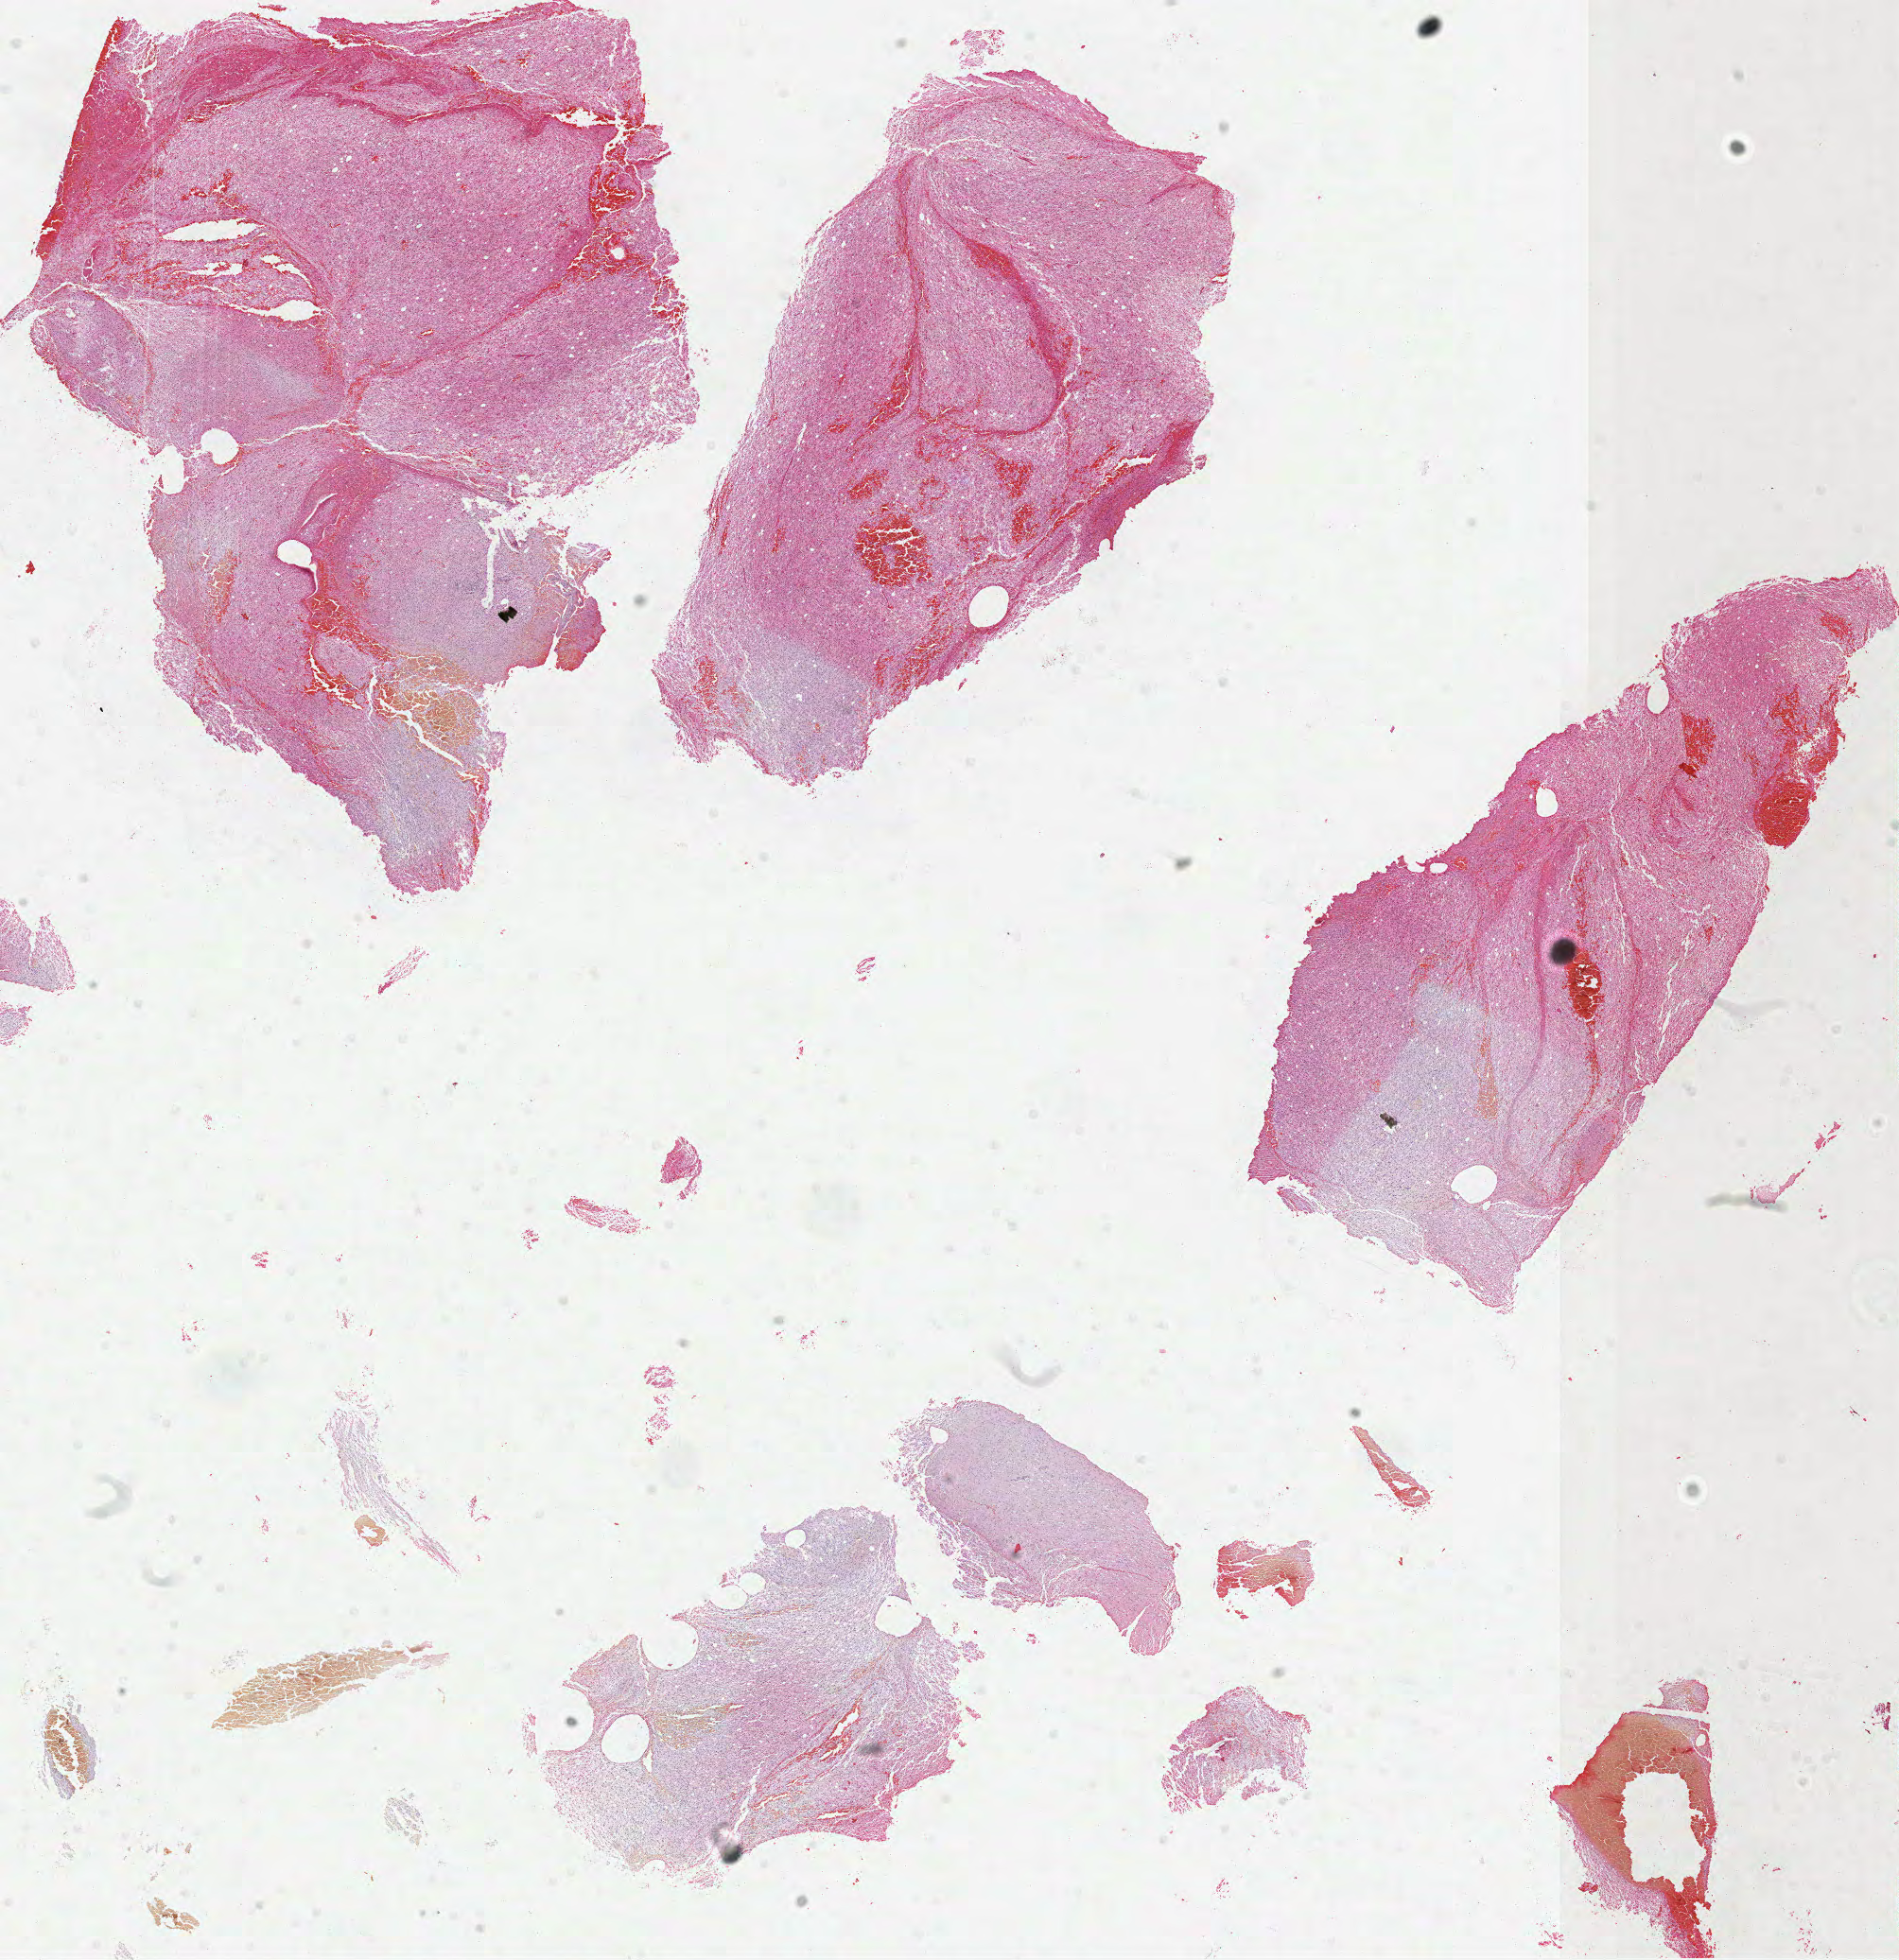
Digitized Hematoxylin and eosin (H&E) stained tissue section (whole slide), whole scanned area (about 16.2 x 16.7 mm, from a 40x scan) shown as a low-resolution overview; formalin-fixed paraffin-embedded (FFPE) diagnostic section; sample: primary tumour, brain. Male, age 35 years at initial diagnosis. Histologic grade: G2 (moderately differentiated).
Laterality: right. Histologic diagnosis: Oligodendroglioma, NOS.